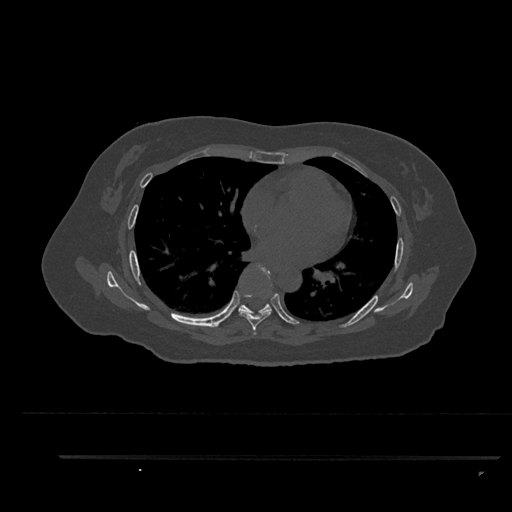
CT including the spine, one axial slice; position 536 of 797 along the scan axis; reconstruction kernel Br40s/3; bone window (W 1800 / L 400 HU); 512 × 512 image matrix, field of view 408 × 408 mm. Female patient, age 44 years. From the clinical record (not read from this slice): primary cancer: renal; vertebrae with lytic lesions (as recorded): L1.
Annotated regions visible in this slice (semi-automatic segmentation, software-assisted and operator-edited):
- T6 vertebra: bounding box (x1, y1, x2, y2) in pixels: (239, 264, 272, 335)
- T7 vertebra: (238, 294, 272, 315)